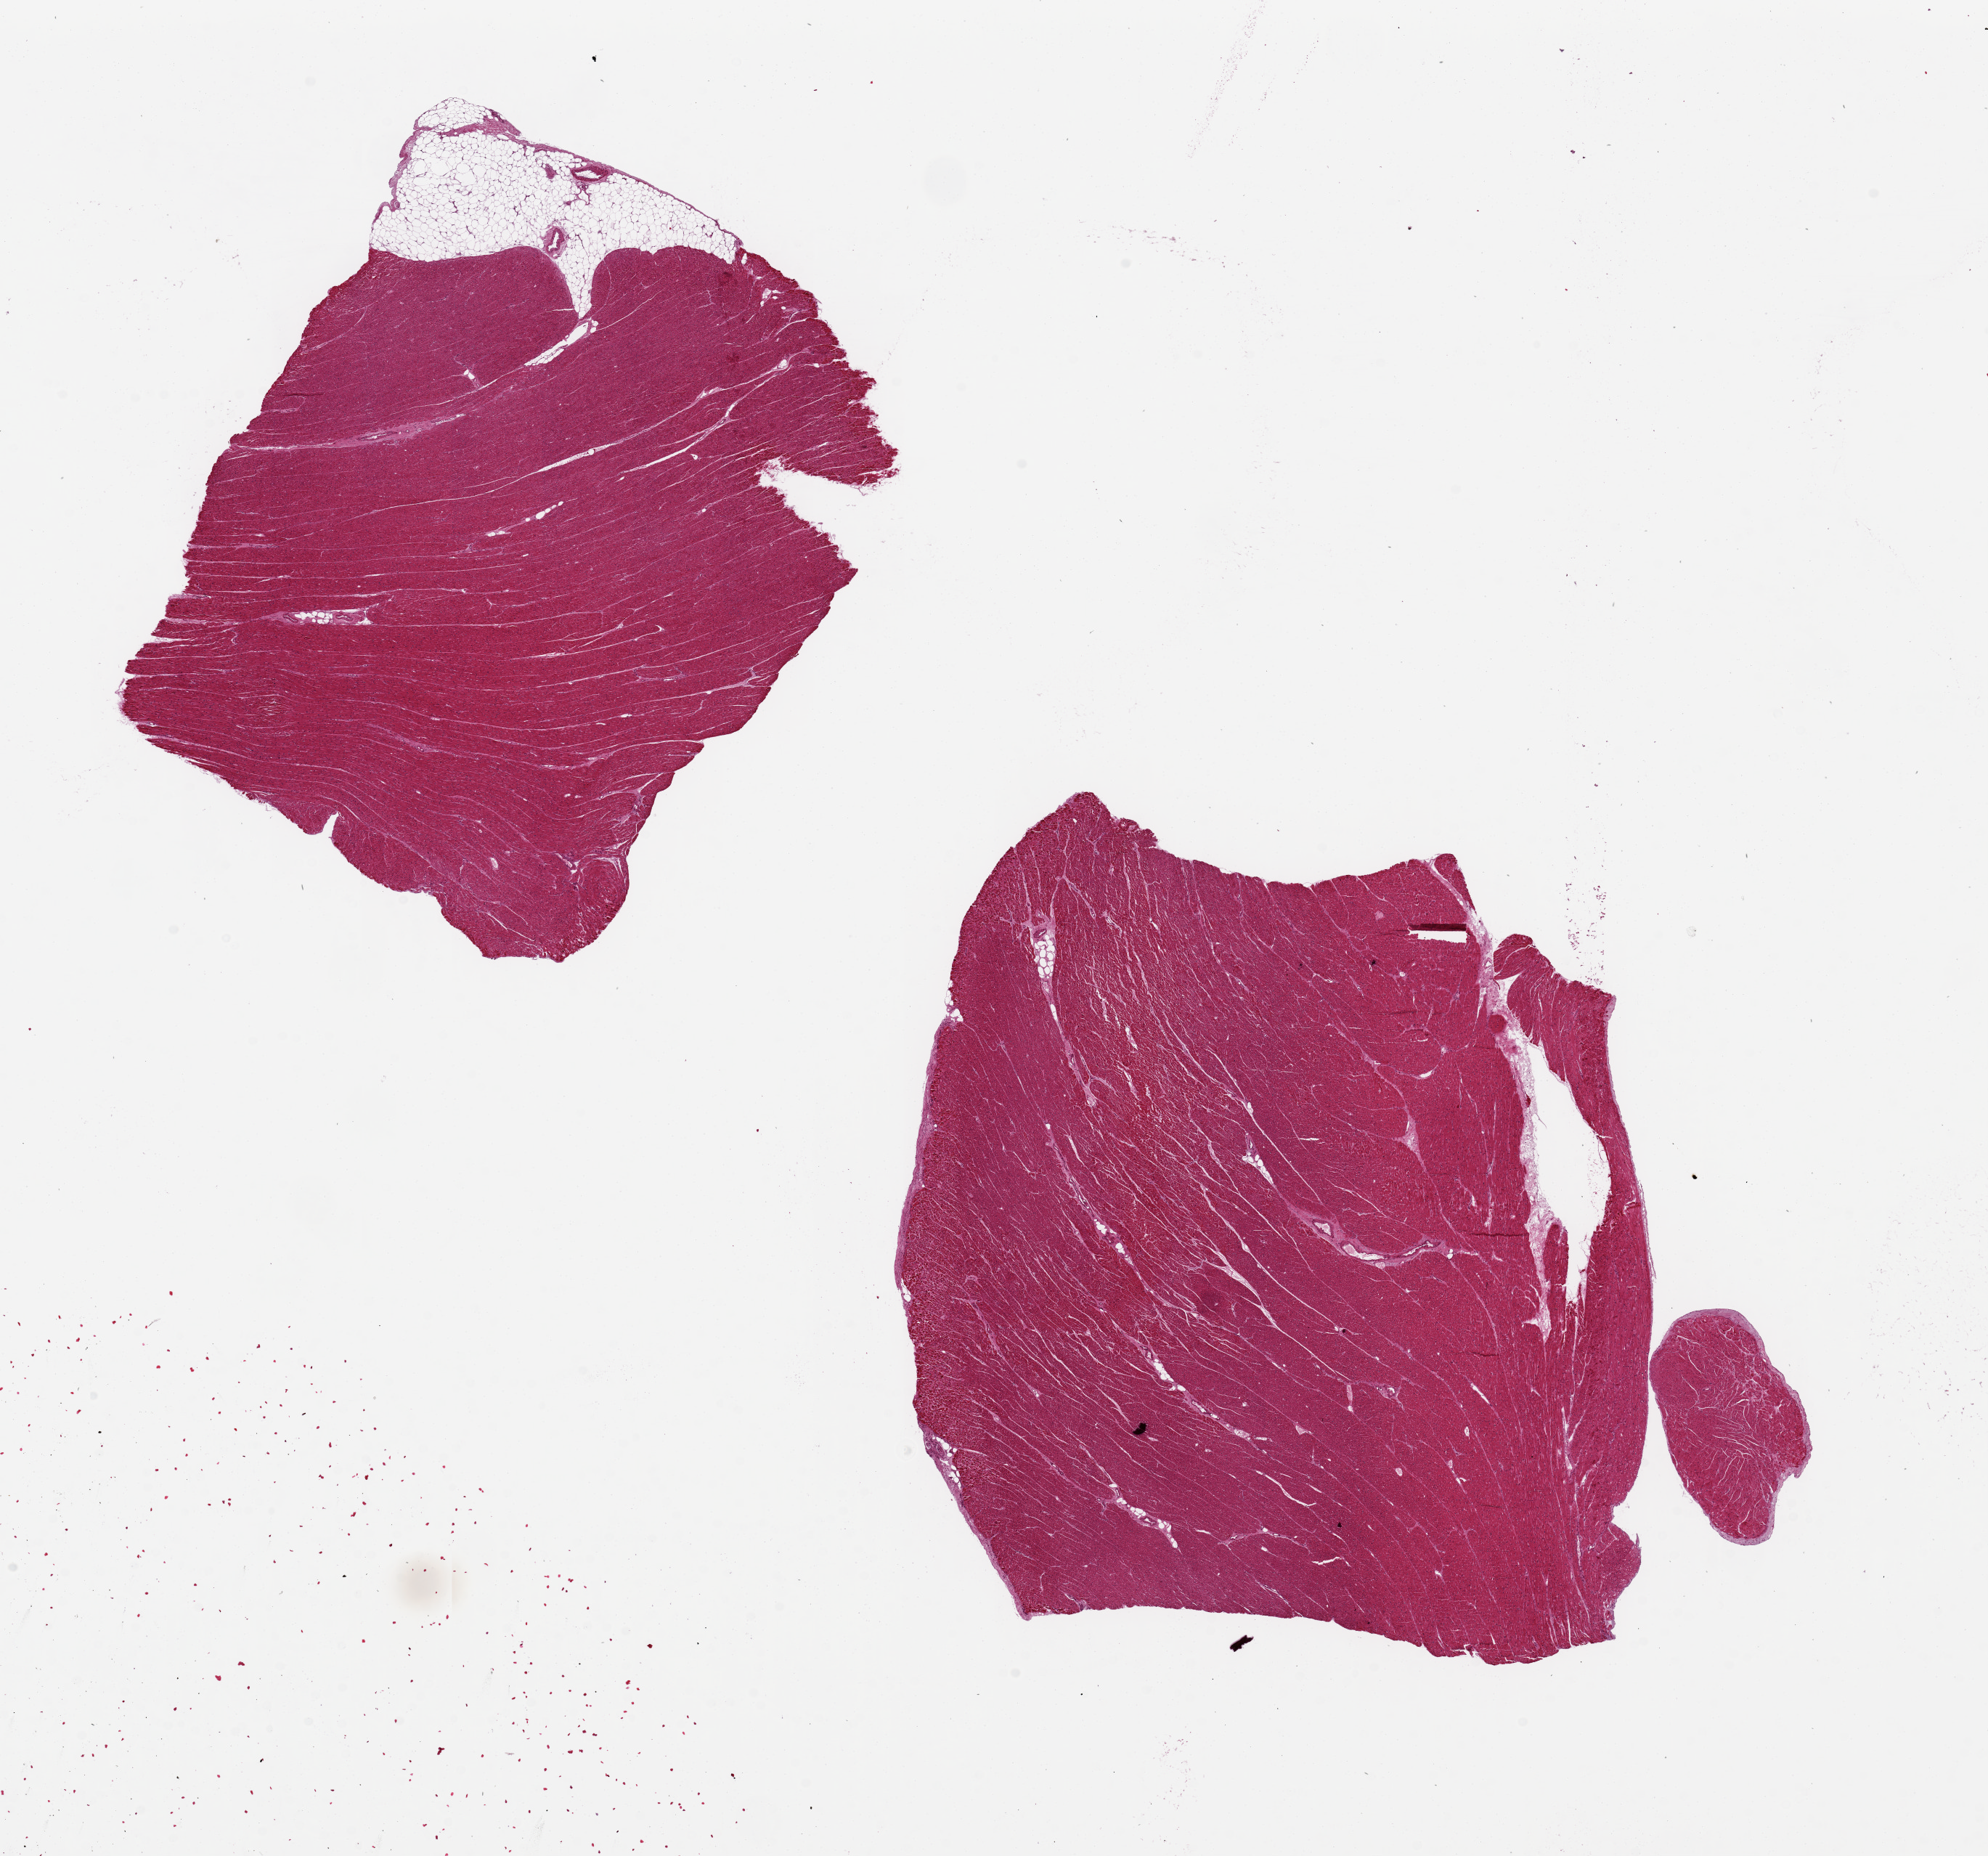
Whole-slide image, H&E stain, brightfield — shown as a low-resolution overview of the whole scanned area (about 21.7 x 20.2 mm, from a 20x scan), PAXgene-fixed paraffin-embedded (PFPE) section, sampled site (target tissue): heart, donor tissue sample. Male donor.
Pathologist's review note for this sample: 2 pieces ~8x7mm; Presumed left ventricle, contraction band ischemic changes noted, several.